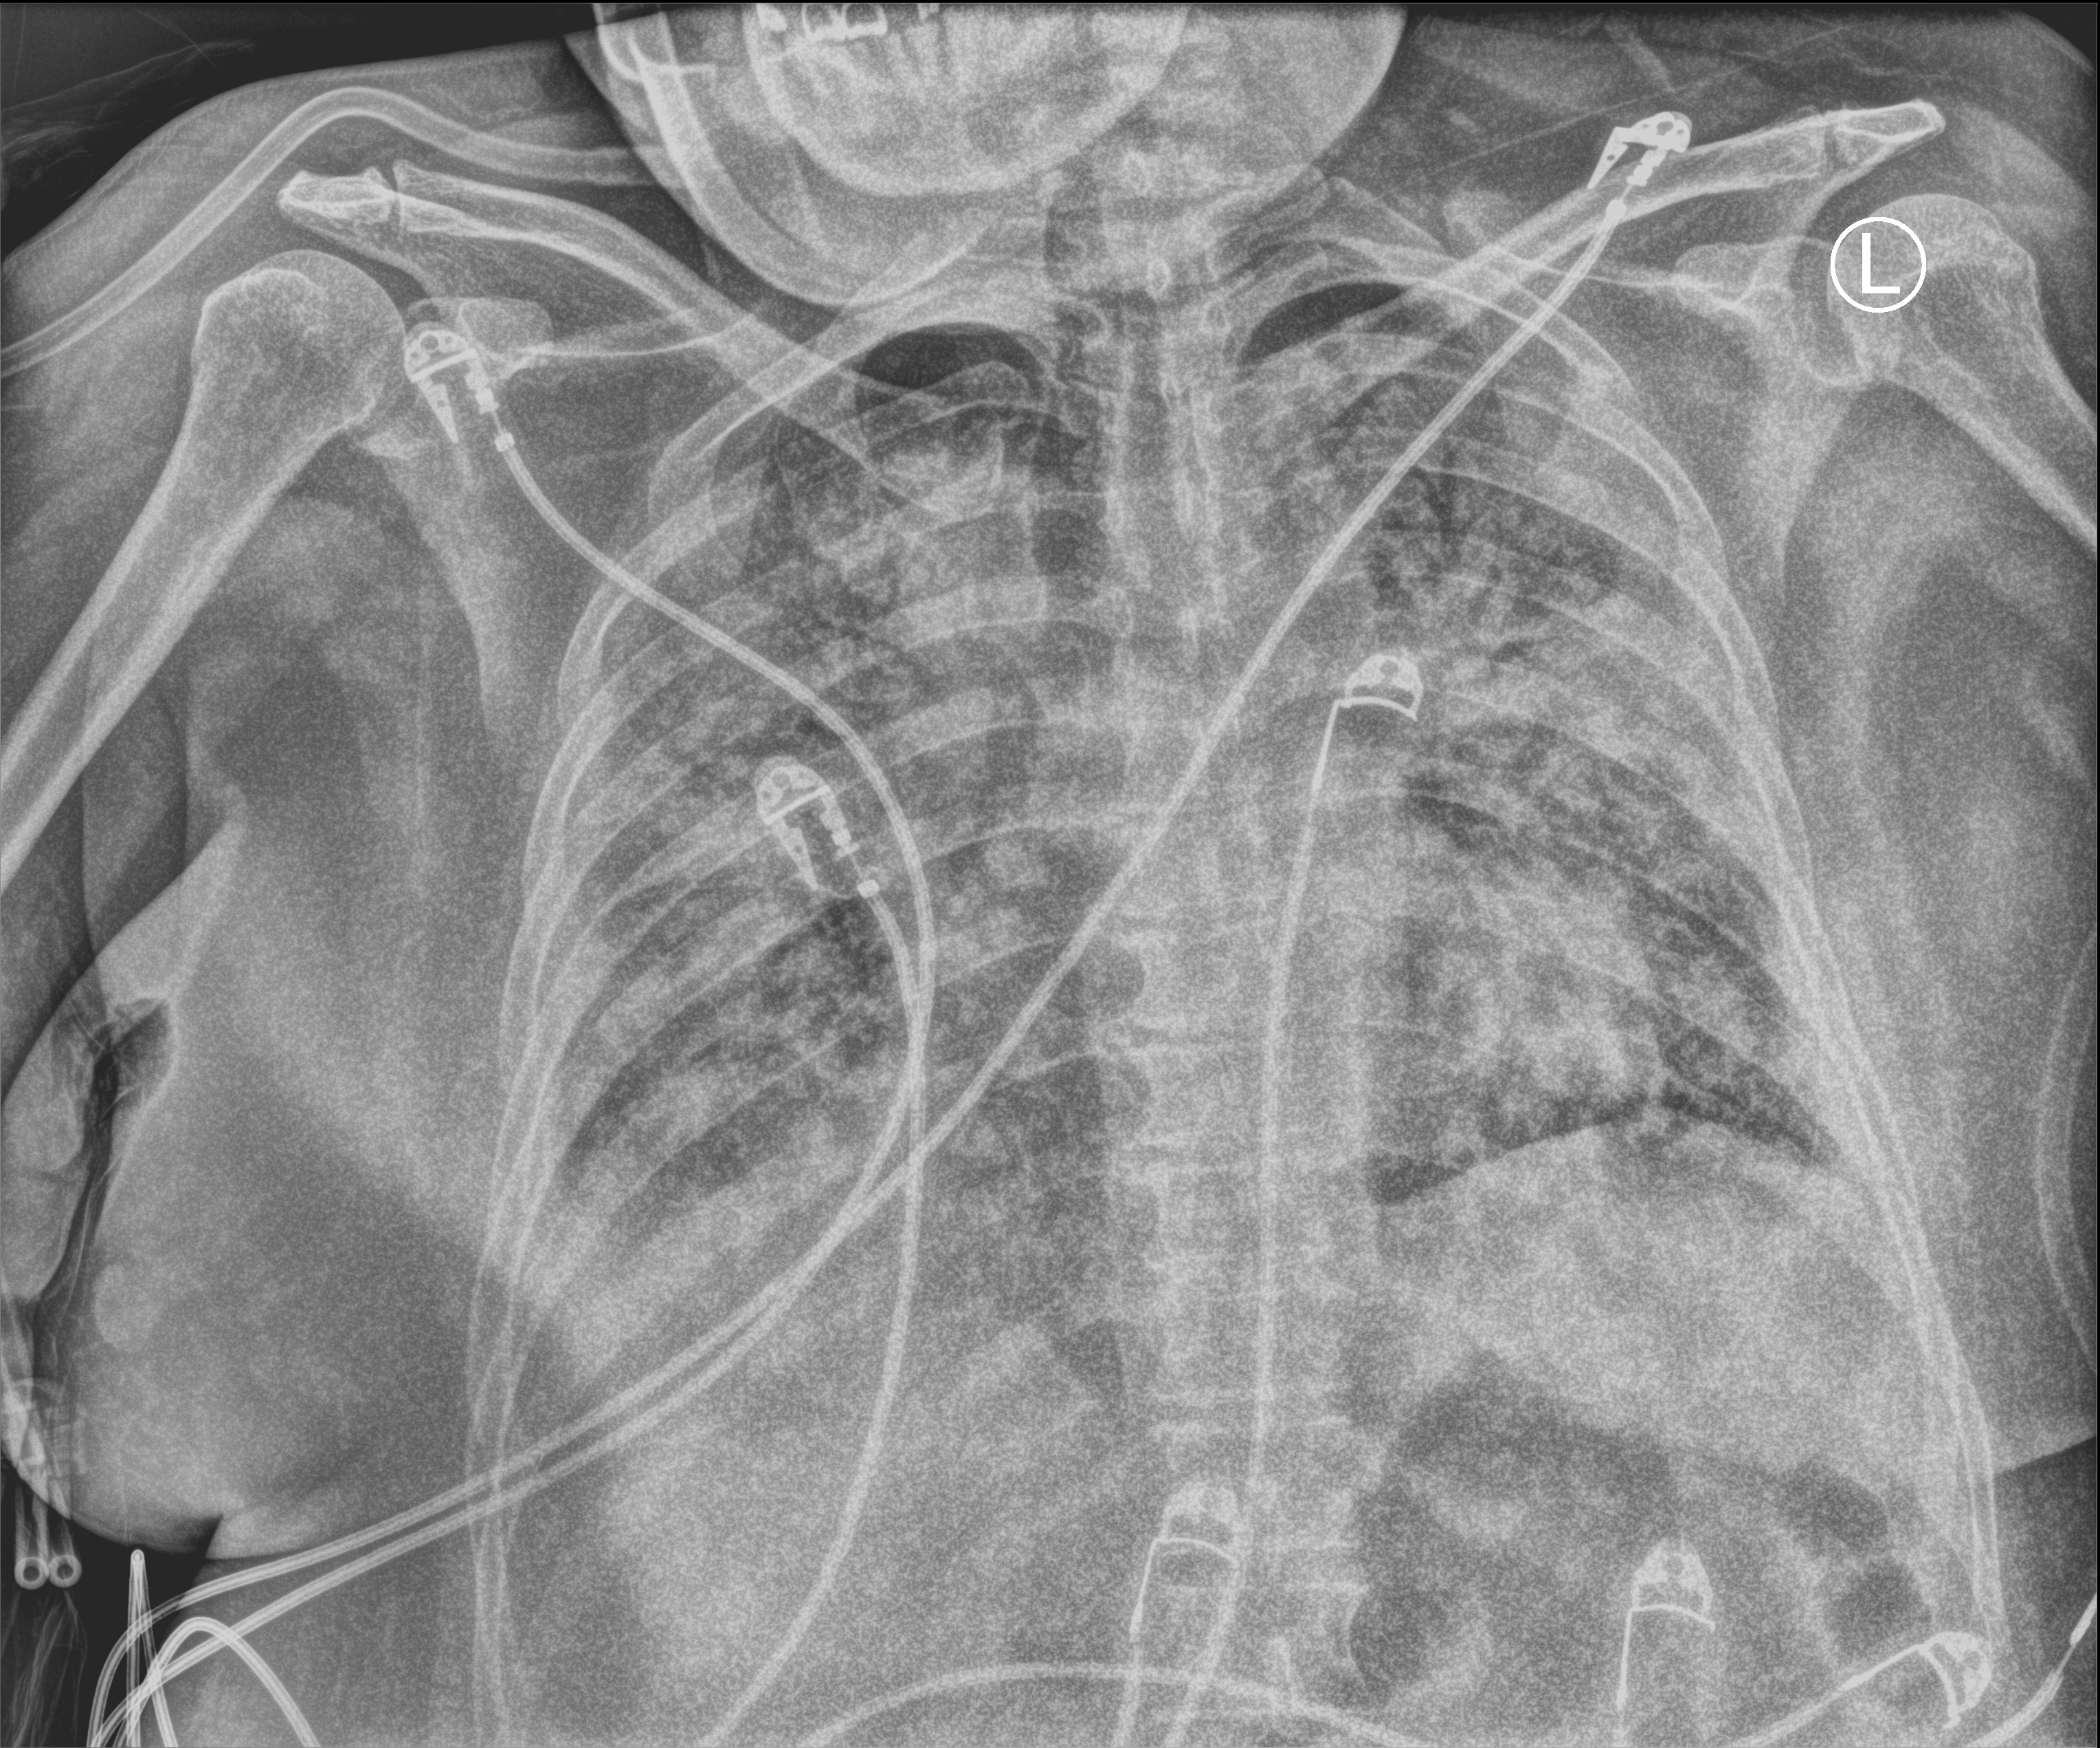
Chest X-ray (portable). Patient hospitalised with COVID-19; female, aged 18–59 years.
From the hospital-stay record, not from the radiograph (when in the stay this image was taken is not recorded):
- chronic kidney disease (admission record): no